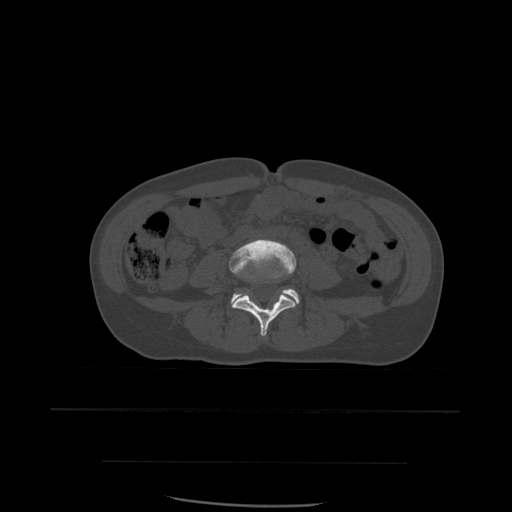
CT including the spine, one axial slice; position 164 of 574 along the scan axis; bone window (W 1800 / L 400 HU); 1.25 mm slice thickness; 512 × 512 image matrix. Patient age 48 years. From the clinical record (not read from this slice): primary cancer: lung; vertebrae with lytic lesions (as recorded): T11.
Structures marked on this image (semi-automatic segmentation, software-assisted and operator-edited):
- L4 vertebra: bounding box (x1, y1, x2, y2) in pixels: (229, 240, 297, 337)
- L5 vertebra: (231, 289, 300, 308)